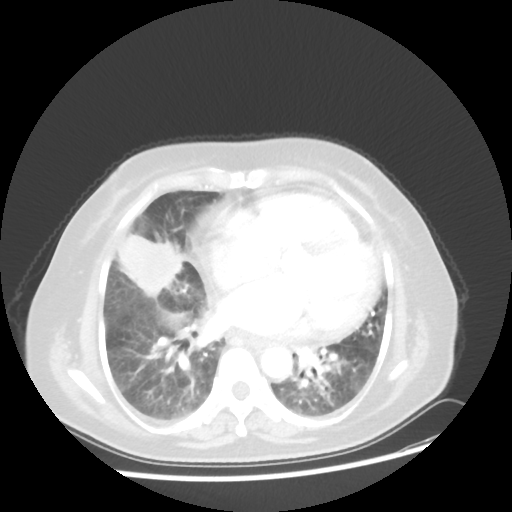
Chest CT, one axial slice. Position 19 of 45 along the scan axis. Reconstruction kernel STANDARD. Lung window (W 1500 / L -600 HU). 5 mm slice thickness. 512 × 512 image matrix. Patient: female, 67 years. Case-level facts recorded for this patient, not image findings: clinical TNM (as recorded): T2a N3 M1a.
Structures marked on this image (rectangle marked by the reading radiologist):
- lung tumour (recorded histology: adenocarcinoma): bounding box <119,228,181,303> (left, top, right, bottom; pixels)